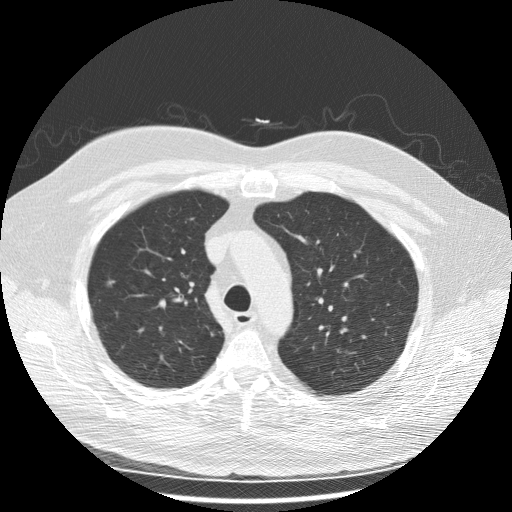
Low-dose screening chest CT, one axial slice. Position 183 of 243 along the scan axis. Lung window (W 1500 / L -600 HU). 2.5 mm slice thickness. 512 × 512 image matrix, field of view 380 × 380 mm.
Outlined on this slice (outlined manually by an expert reader):
- lesion 1 (tumor, upper lobe of right lung): bounding box (x1, y1, x2, y2) in pixels: (107, 280, 115, 285)